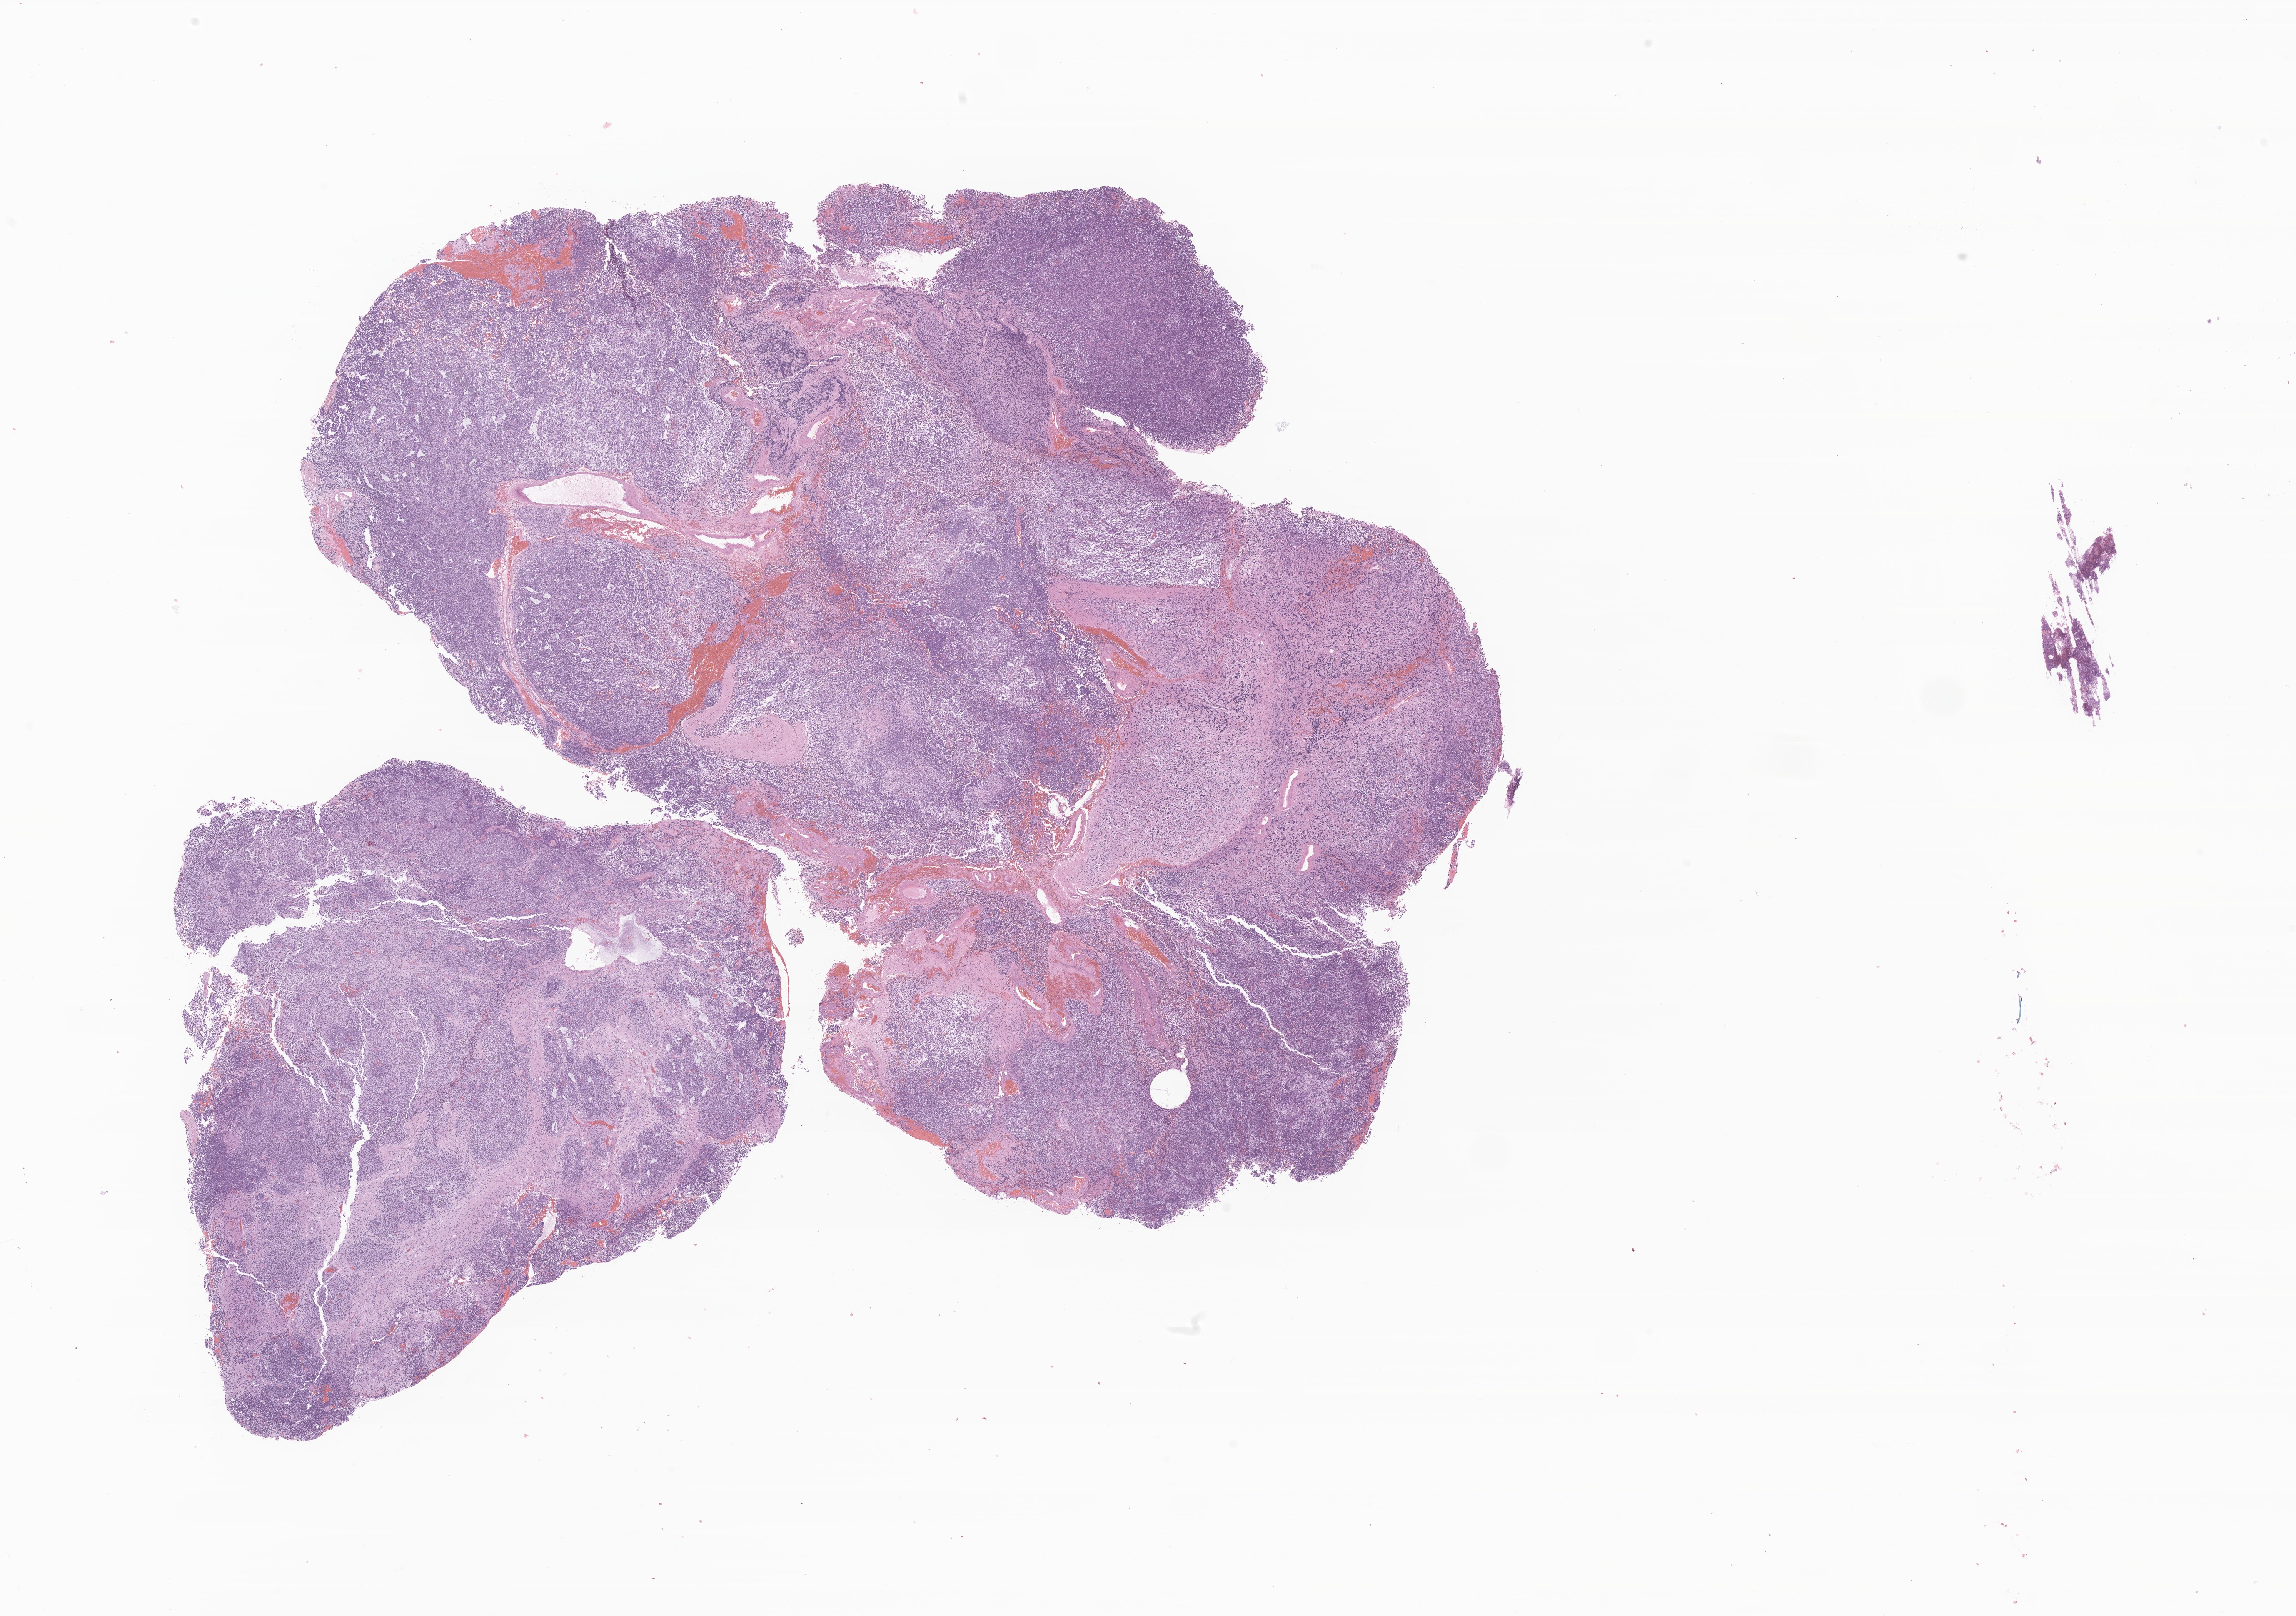
Digitized hematoxylin and eosin (H&E)-stained section of tumor tissue from the brain, whole scanned area (about 25.2 x 17.7 mm) shown as a low-resolution overview, formalin-fixed, paraffin-embedded (FFPE) tissue. Patient: male, age 63 months (5 years 3 months).
Diagnosis: Tumor cells, uncertain whether benign or malignant.